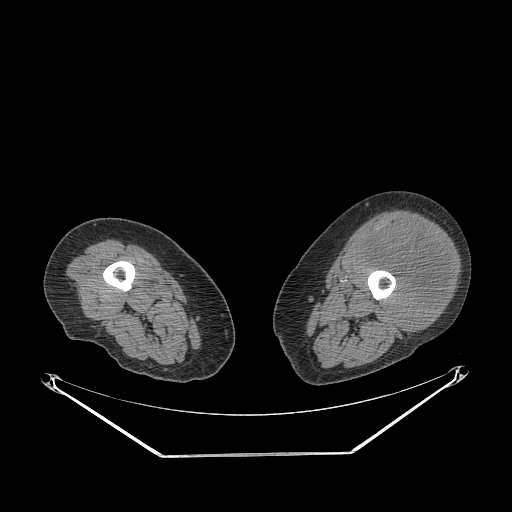
CT of an extremity soft-tissue mass (from a PET/CT study), one axial slice. Slice 216 of 267 in the series (ordered by position). Reconstruction kernel STANDARD. Soft-tissue window (W 400 / L 40 HU). 512 × 512 image matrix. Female patient. Case-level facts recorded for this patient, not image findings: histological type: undifferentiated – high grade; grade: high; site of the primary tumour: left thigh.
Outlined on this slice (expert contour drawn on MRI and transferred to this co-registered scan by the dataset authors):
- gross tumour volume including surrounding oedema: bounding box [x1, y1, x2, y2] px = [359, 222, 453, 330]
- gross tumour volume (mass): [361, 222, 451, 330]